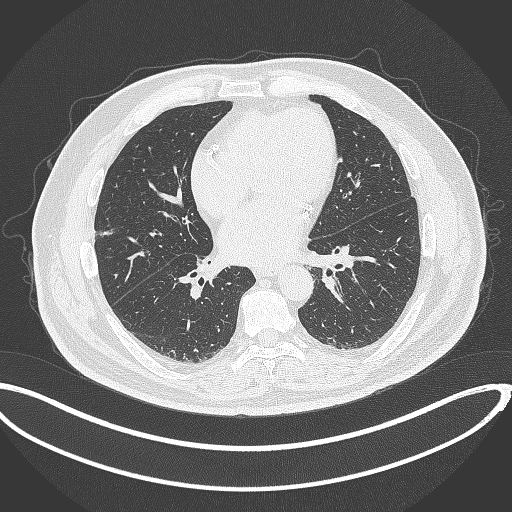
Chest CT, one axial slice; reconstruction kernel B70f; 120 kVp; lung window (W 1500 / L -600 HU); 1 mm slice thickness; 512 × 512 image matrix, field of view 427 × 427 mm. Male patient, age 68 years. Case-level facts recorded for this patient, not image findings: clinical TNM (as recorded): T1c N0 M0.
Annotated regions visible in this slice (rectangle marked by the reading radiologist):
- lung tumour (recorded histology: adenocarcinoma): box from (x=97, y=227) to (x=119, y=240) px